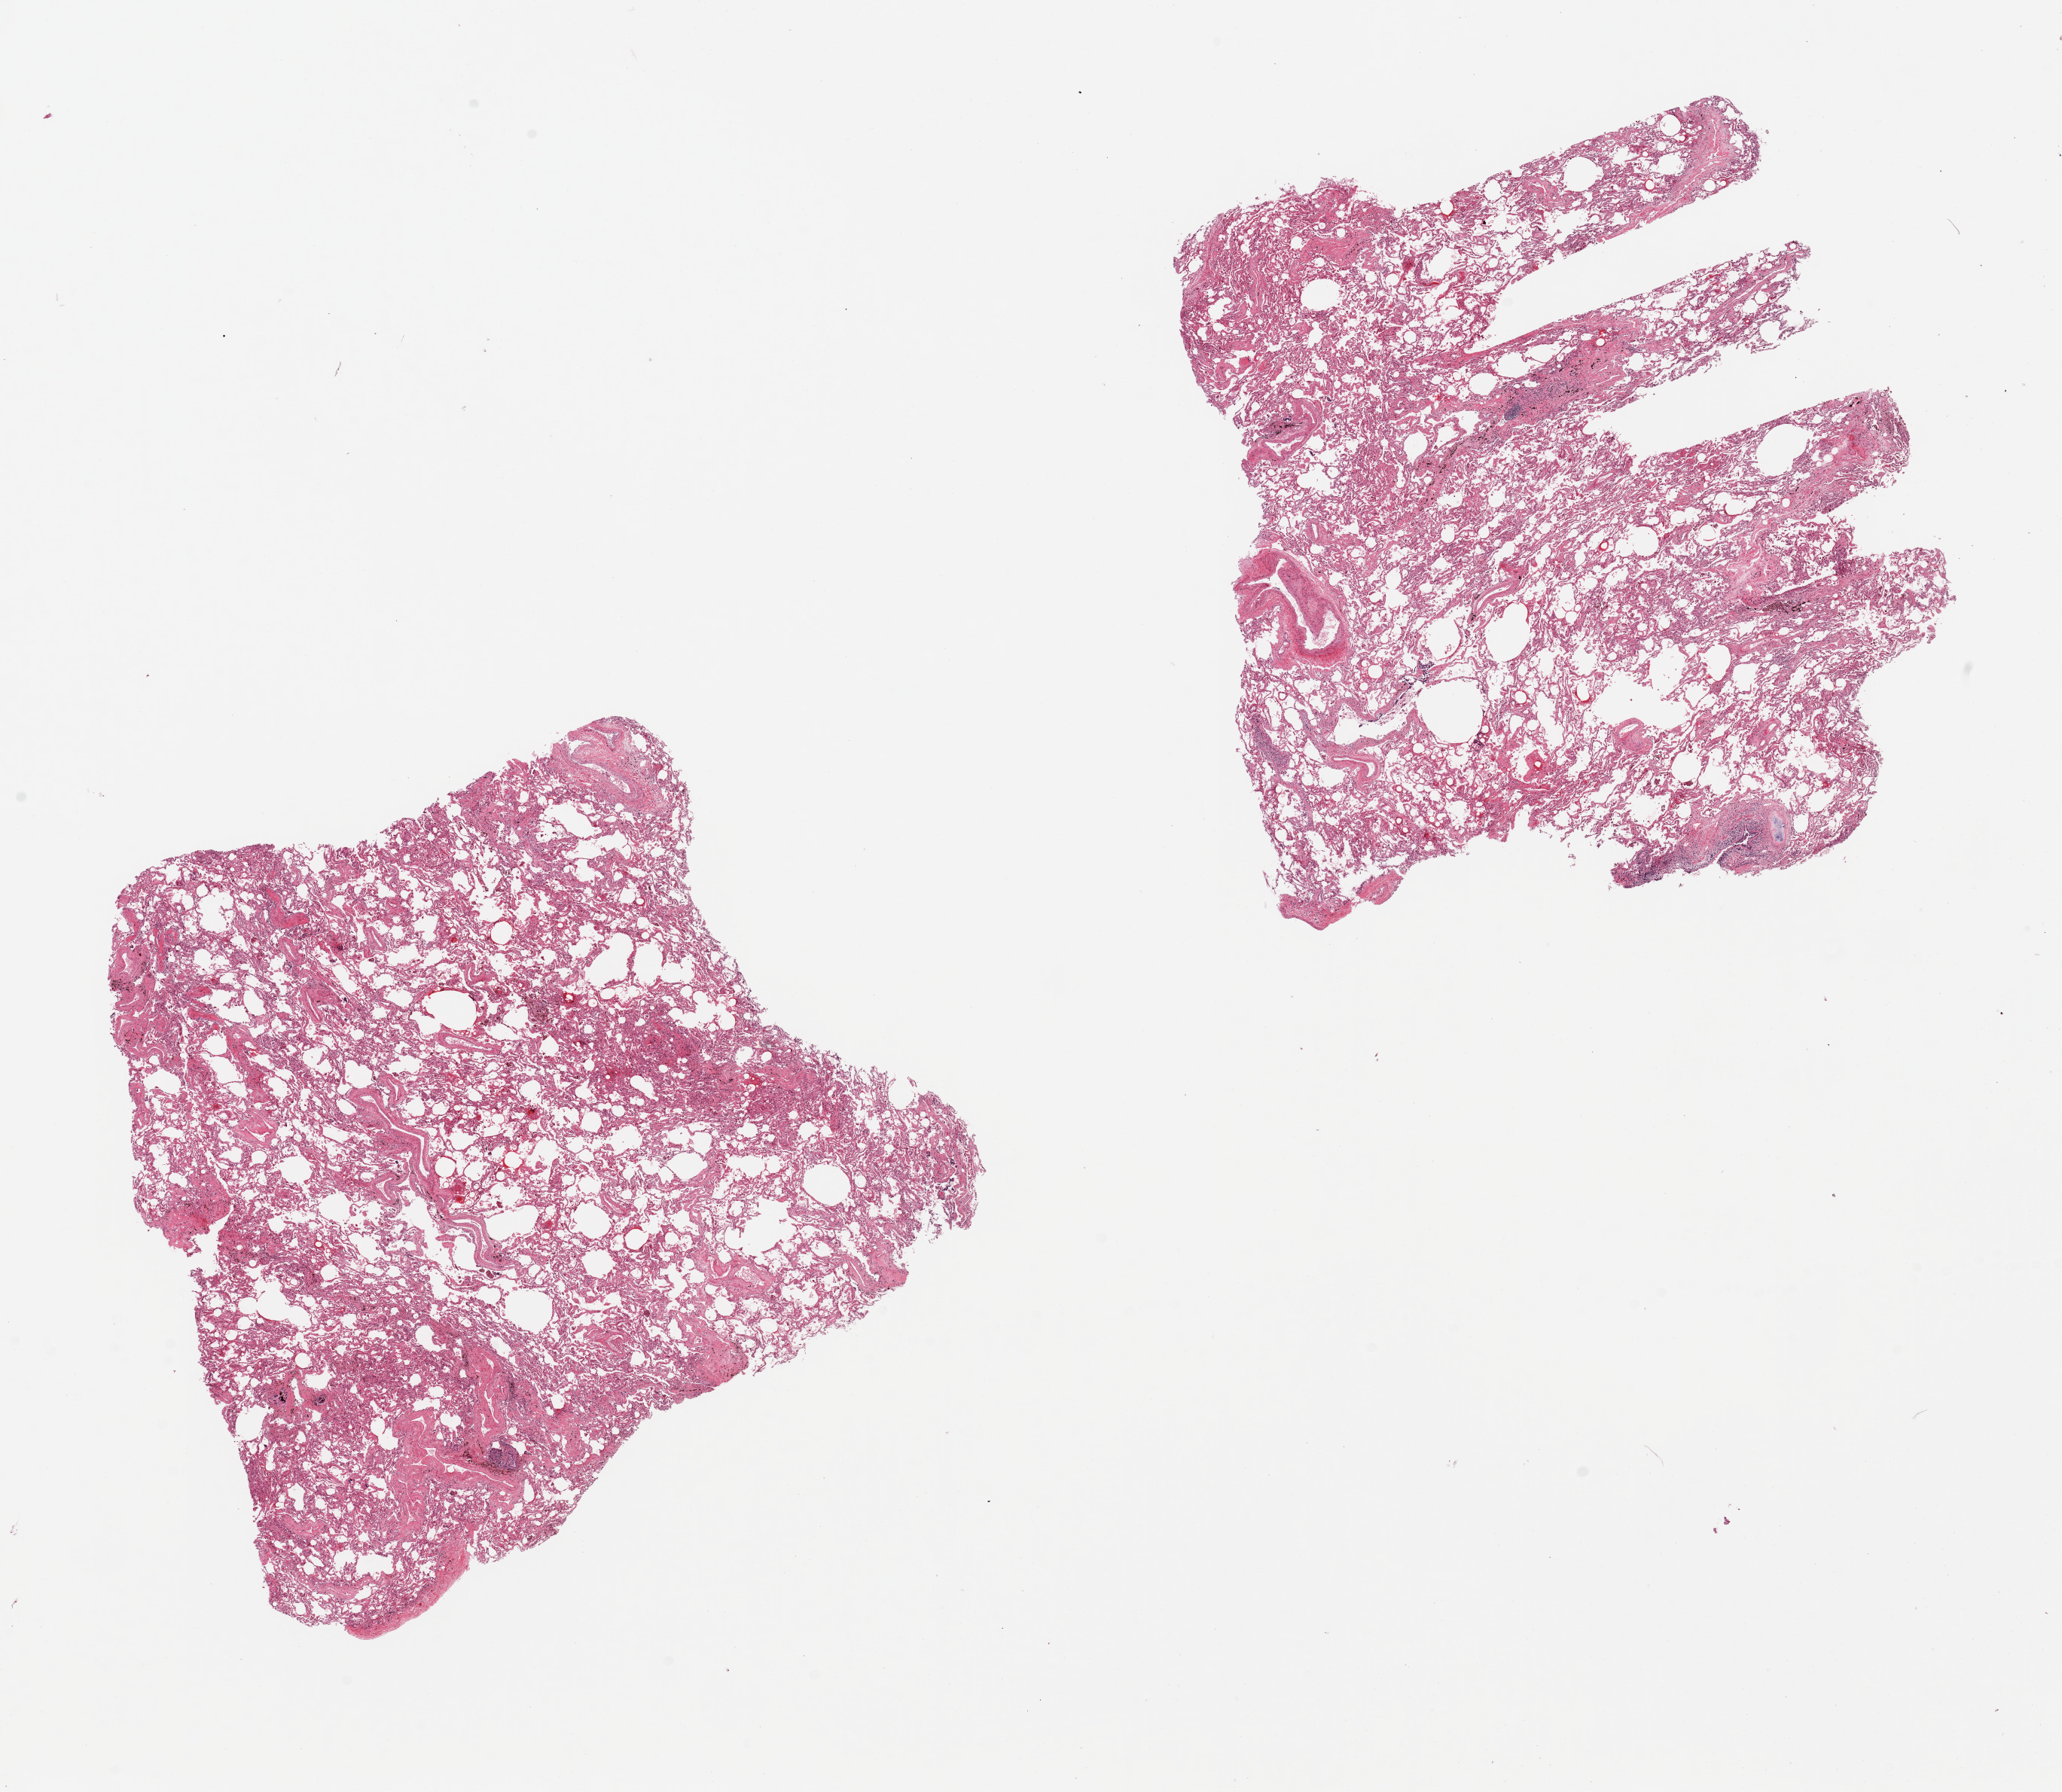
Digitized H&E-stained section, brightfield — shown as a low-resolution overview of the whole scanned area (about 21.7 x 18.8 mm, from a 20x scan). PAXgene-fixed paraffin-embedded (PFPE) section. Section of lung (target tissue). Donor tissue sample. Donor sex: male.
* reviewer comment on this tissue sample: 2 pieces, patchy congestion, emmphysematous changes, bronchiolitis